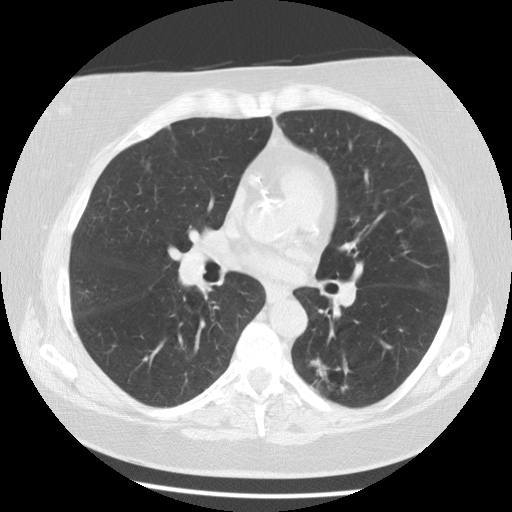
Low-dose screening chest CT, one axial slice; position 61 of 116 along the scan axis; 120 kVp; lung window (W 1500 / L -600 HU); 512 × 512 image matrix, field of view 341 × 341 mm.
Structures marked on this image (manually delineated by an expert):
- lesion 1 (tumor, lower lobe of left lung): box from (x=312, y=359) to (x=327, y=378) px